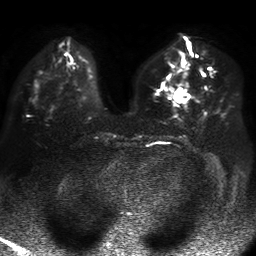
Breast MRI, one axial slice. Position 23 of 50 along the scan axis. Diffusion-weighted series; image 2 of 4 stored at this slice position (different b-values; order by instance number). 1.5 T. 256 × 256 image matrix, field of view 360 × 360 mm. Female patient.
Structures marked on this image (outlined manually by an expert reader):
- tumour on diffusion-weighted imaging: bounding box (x1, y1, x2, y2) in pixels: (175, 88, 189, 103)